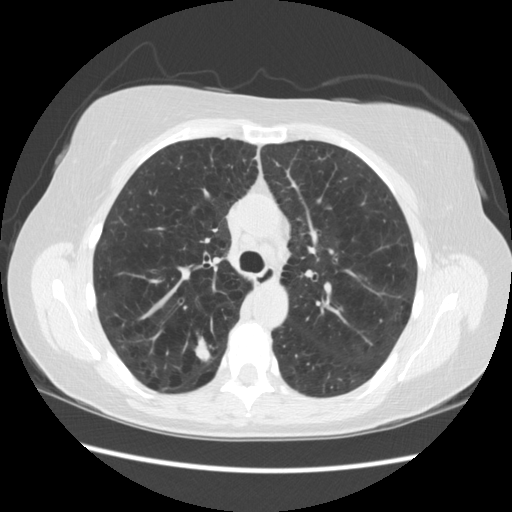
Low-dose screening chest CT, axial slice, third screening round (two years after baseline), lung window (W 1500 / L -600 HU), 2.5 mm slice thickness, standard (soft-tissue) reconstruction kernel (STANDARD), slice 78 of 235 in the series, 512 × 512 image matrix, field of view 360 × 360 mm. Female participant, aged 55 years at enrolment. Current smoker at enrolment.
- Expert reader's lesion annotation, bounding box [x1, y1, x2, y2] px = [176, 328, 227, 376].
- Reader record for this screening exam (exam-level; its link to the box is not recorded): non-calcified nodule or mass ≥4 mm, right upper lobe, 11 × 11 mm, poorly defined margins, soft tissue attenuation, pre-existing on the prior screen: no.
- Official screen result: positive, other.
- Participant outcome: lung cancer diagnosed 96 days after this screen — small cell carcinoma, NOS, right upper lobe.